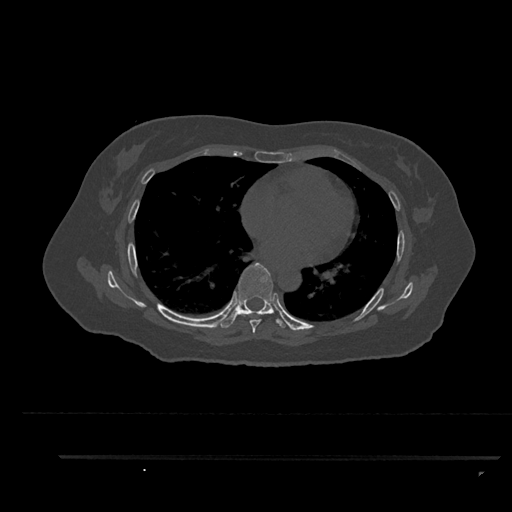
CT including the spine, one axial slice; position 529 of 797 along the scan axis; reconstruction kernel Br40s/3; bone window (W 1800 / L 400 HU); 0.5 mm slice thickness; 512 × 512 image matrix. Patient: female, 44 years. From the clinical record (not read from this slice): primary cancer: renal.
Annotated regions visible in this slice (semi-automatically segmented with operator editing):
- T6 vertebra: box from (x=244, y=314) to (x=262, y=333) px
- T7 vertebra: (x=219, y=262)–(x=288, y=328)